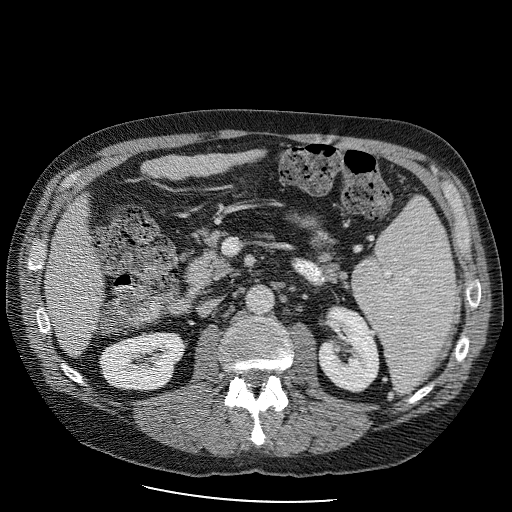
Contrast-enhanced abdominal CT (liver protocol), one axial slice. Slice 33 of 98 in the series (ordered by position). Reconstruction kernel STANDARD. 120 kVp. Soft-tissue window (W 400 / L 40 HU). 2.5 mm slice thickness. 512 × 512 image matrix. From the clinical record (not read from this slice): diagnosis: hepatocellular carcinoma (patient treated with transarterial chemoembolisation; whether this scan precedes or follows treatment is not stated here); TNM stage (as recorded): Stage-II; Child-Pugh class: B; tumour differentiation: moderately differentiated; tumour nodularity: uninodular.
Annotated regions visible in this slice (semi-automatic segmentation, software-assisted and operator-edited):
- liver parenchyma outside the tumour (the mass and vessels are separate outlines, so this box may not span the whole liver): box from (x=44, y=142) to (x=274, y=352) px
- liver vessels: (x=80, y=302)–(x=84, y=305)